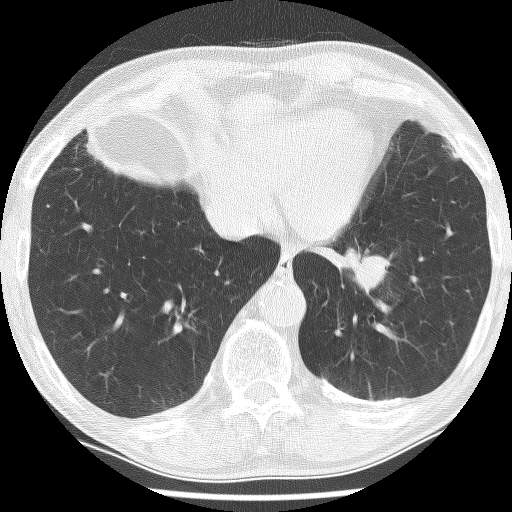
Axial slice from a low-dose chest CT screening exam, baseline screening round, lung window (W 1500 / L -600 HU), slice 184 of 226 in the series, 512 × 512 image matrix. Male participant, aged 74 years at enrolment. Current smoker at enrolment.
Expert reader's lesion annotation, bounding box <312,216,412,308> (left, top, right, bottom; pixels). Reader record for this screening exam (exam-level; its link to the box is not recorded): non-calcified nodule or mass ≥4 mm, left lower lobe, 30 × 27 mm, spiculated (stellate) margins, soft tissue attenuation. Later outcome: lung cancer diagnosed 151 days after this screen — adenocarcinoma, NOS, left lower lobe, stage IIIA (AJCC 6th edition), 49 mm at pathology.